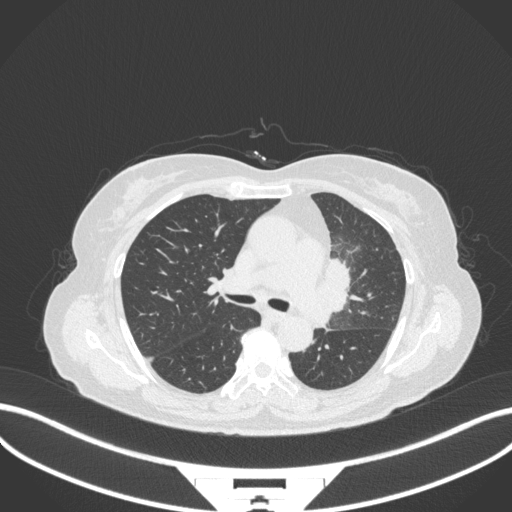
Chest CT, one axial slice. Slice 207 of 382 in the series (ordered by position). 120 kVp. Lung window (W 1500 / L -600 HU). 1 mm slice thickness. 512 × 512 image matrix, field of view 400 × 400 mm. Female patient, age 64 years. Case-level facts recorded for this patient, not image findings: clinical TNM (as recorded): T2a N2 M0.
Structures marked on this image (bounding box drawn by a radiologist):
- lung tumour (recorded histology: adenocarcinoma): bounding box (x1, y1, x2, y2) in pixels: (315, 257, 356, 329)